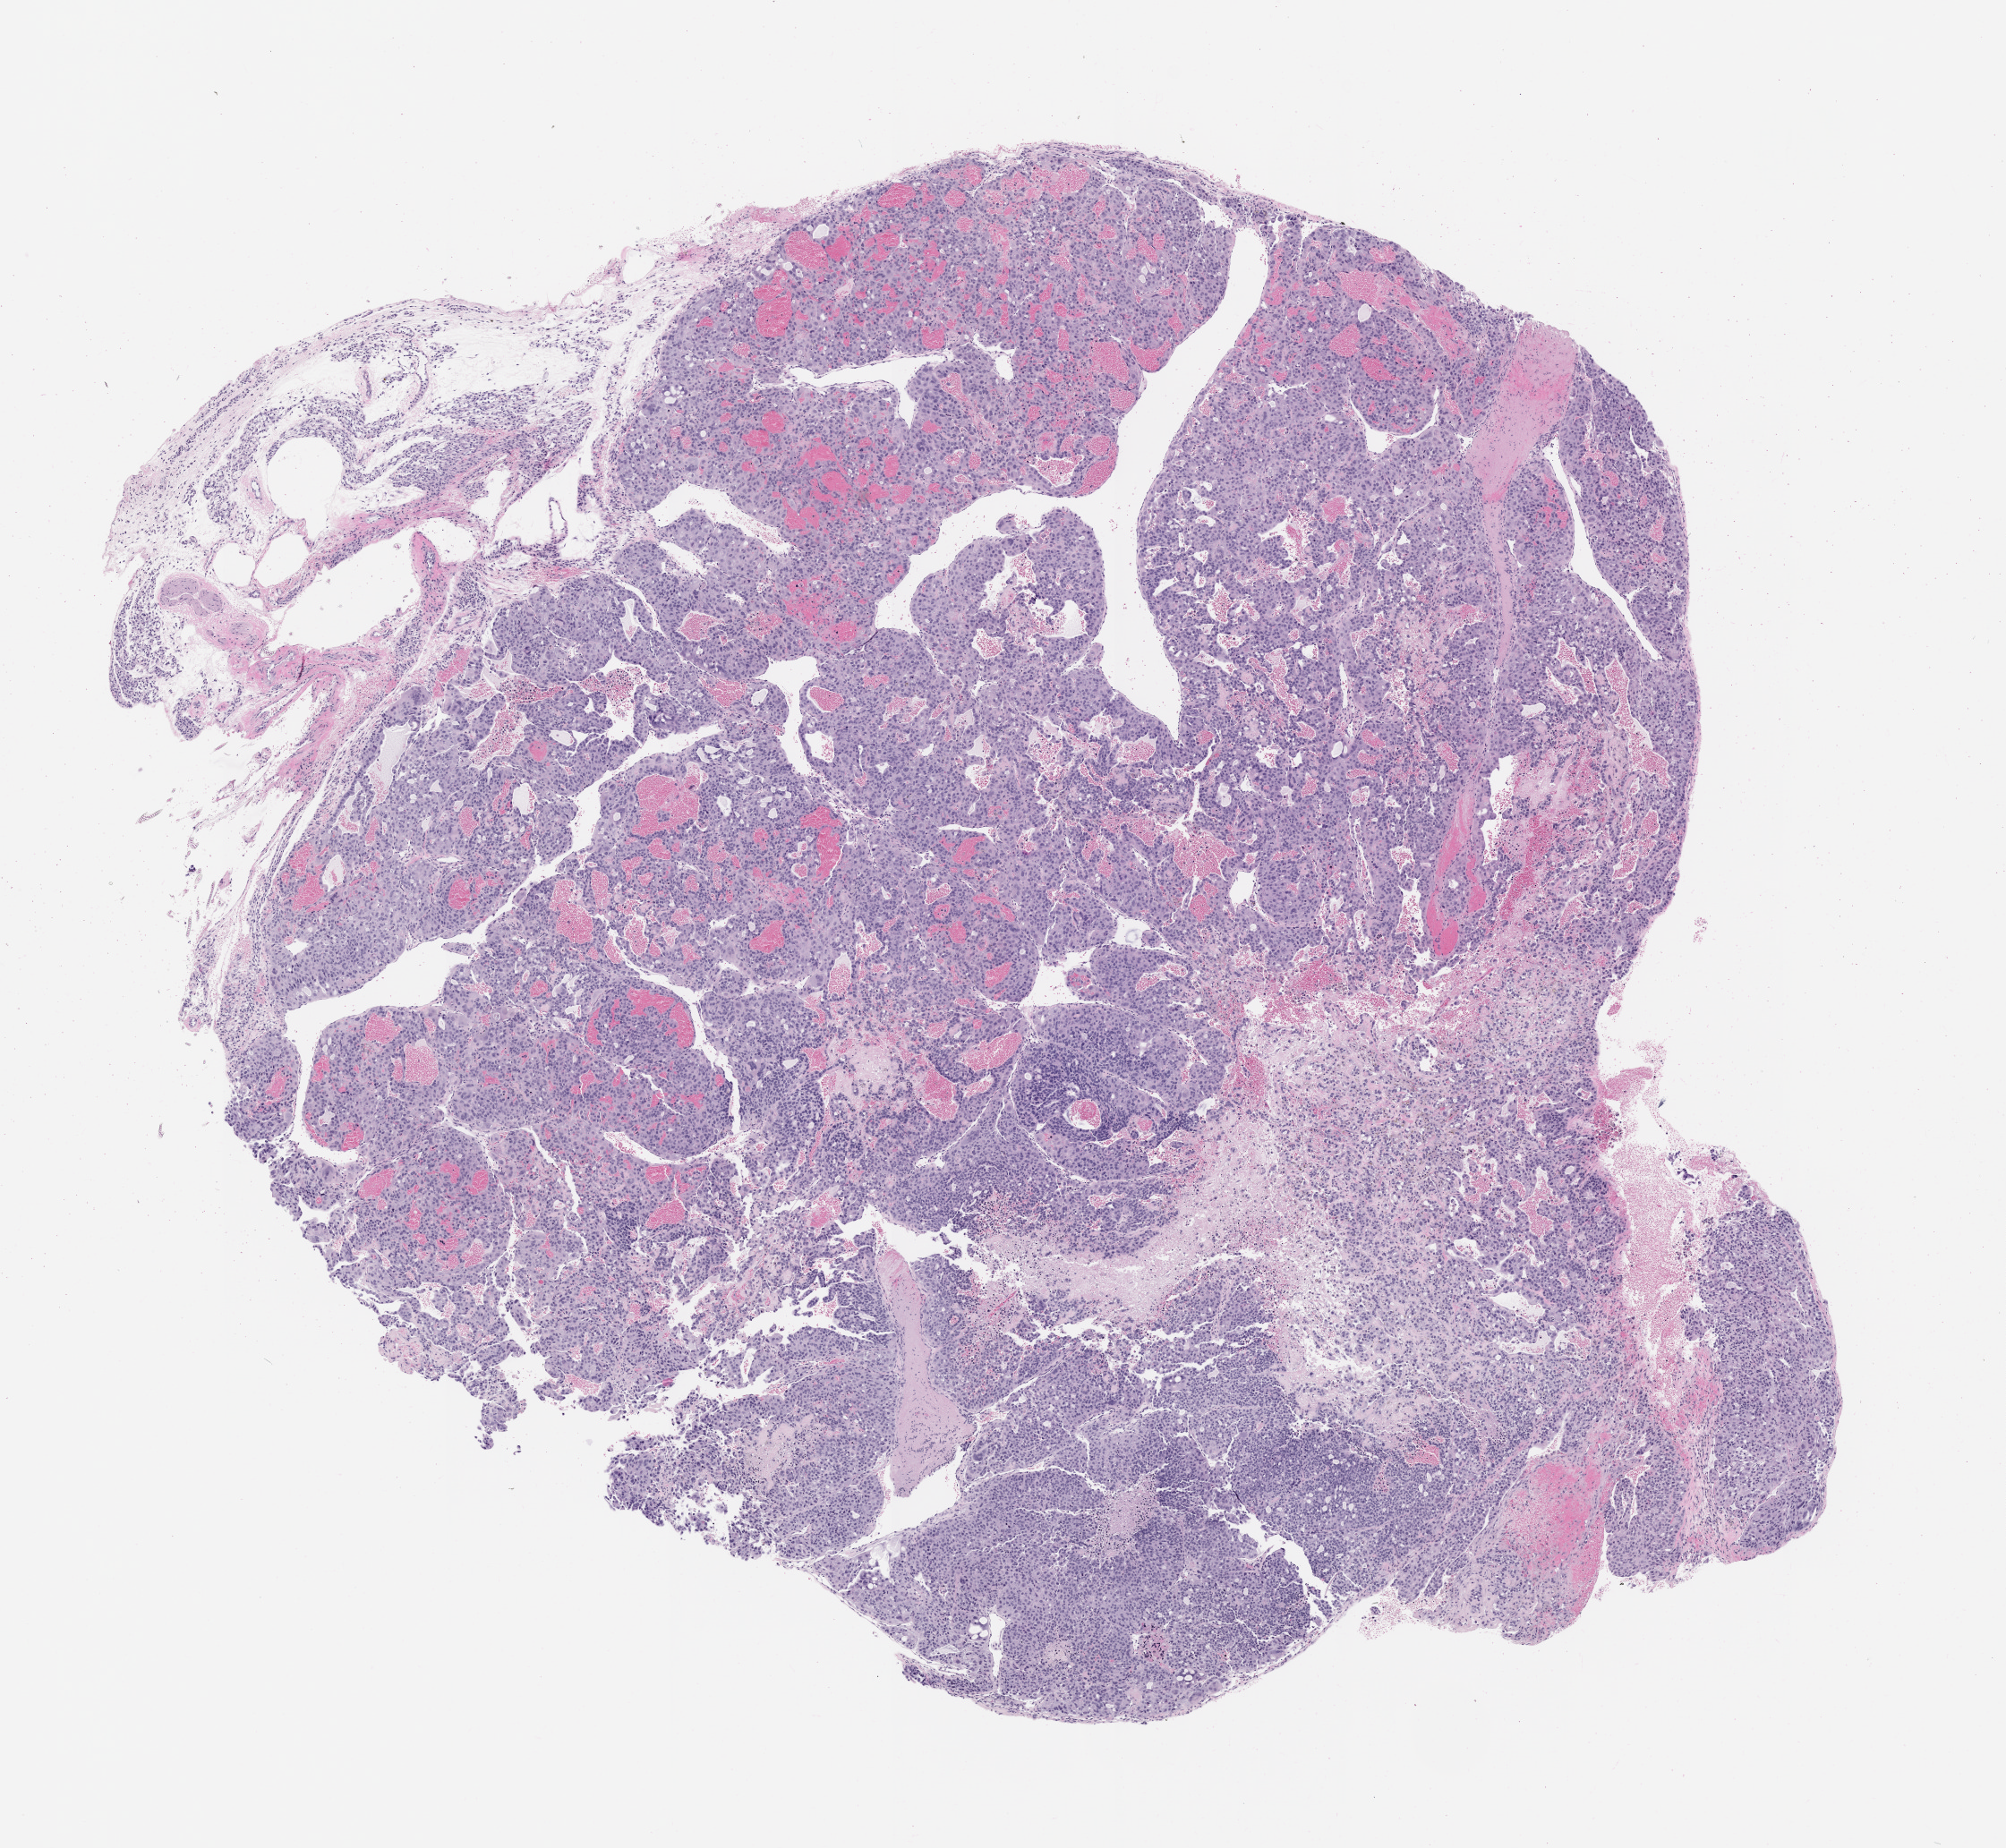
Whole-slide image, hematoxylin and eosin (H&E): patient-derived xenograft (human tumor grown in a mouse), passage 1, low-resolution overview of the scanned area, about 9.0 x 8.3 mm; FFPE section; originating tumor site category: bladder.
Originating patient diagnosis: Urothelial Carcinoma.